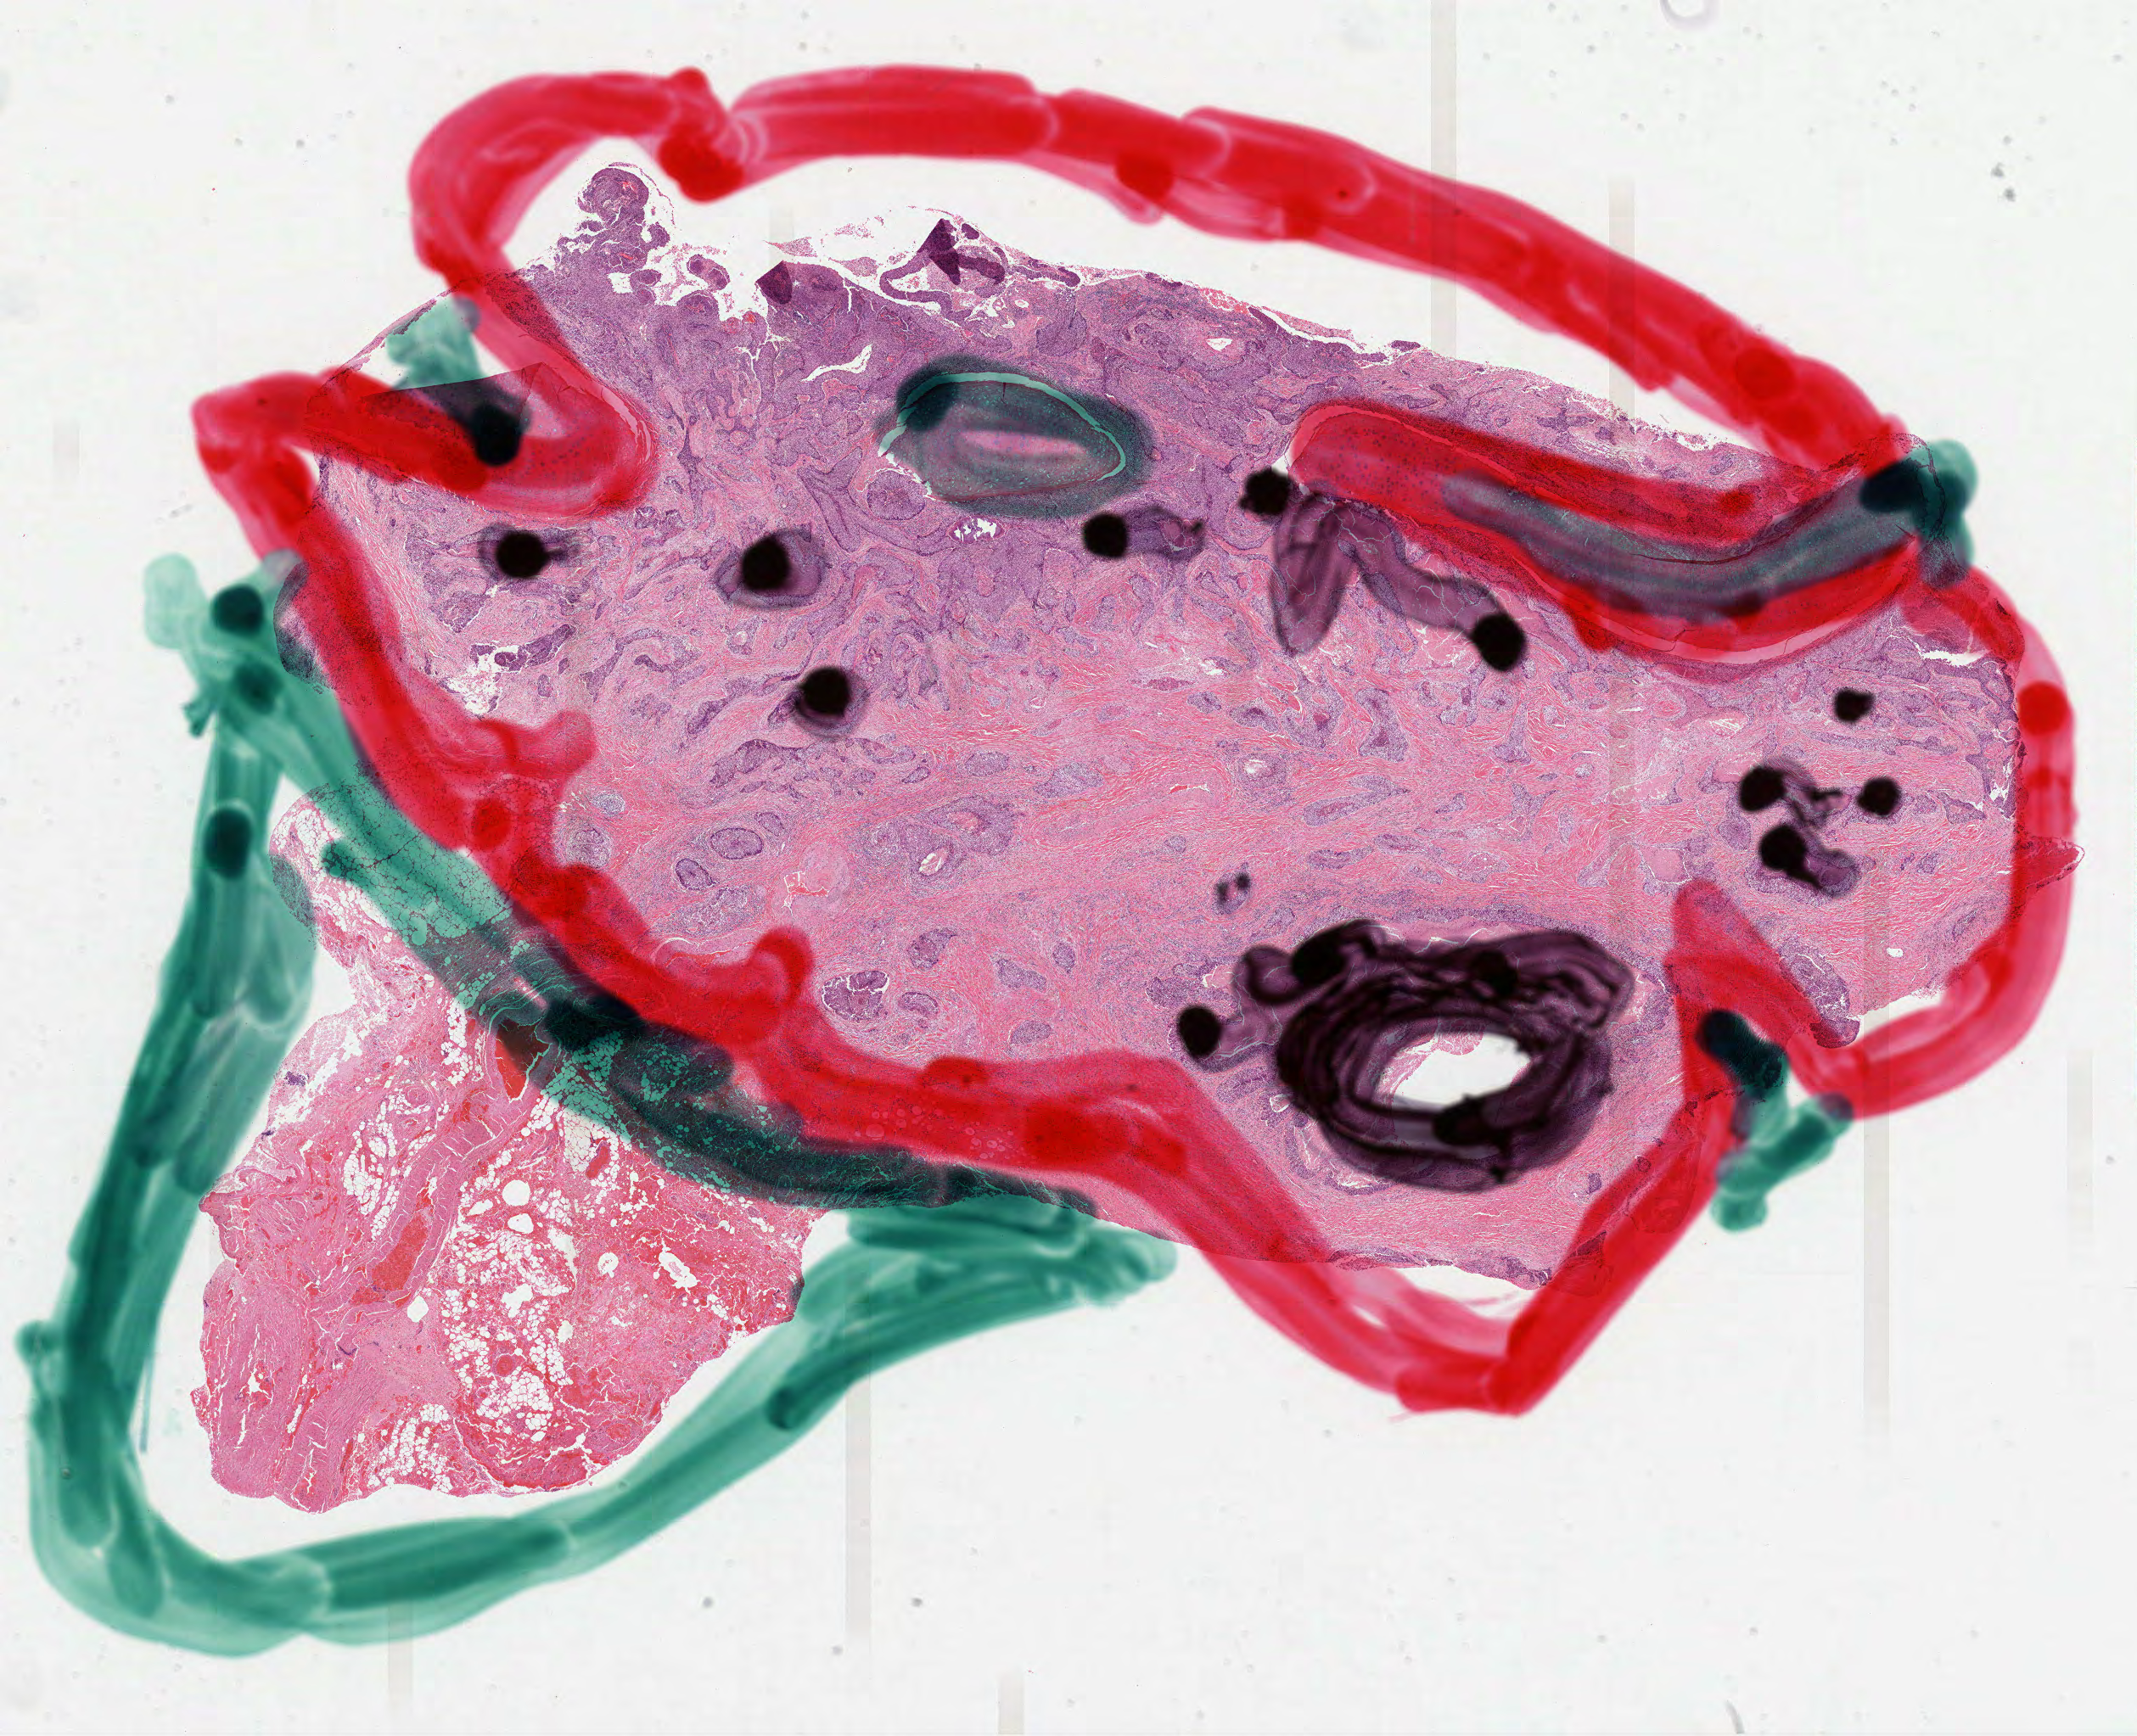
Digitized H&E-stained tissue section (whole slide) — a low-resolution overview of the entire scanned area, about 20.3 x 16.5 mm. Formalin-fixed paraffin-embedded (FFPE) diagnostic section. Lung, primary tumour sample. Male patient; age at initial diagnosis 70 years.
AJCC pathologic stage: IIA (7th edition). Laterality: right. Histologic diagnosis: Squamous cell carcinoma, NOS (middle lobe, lung).